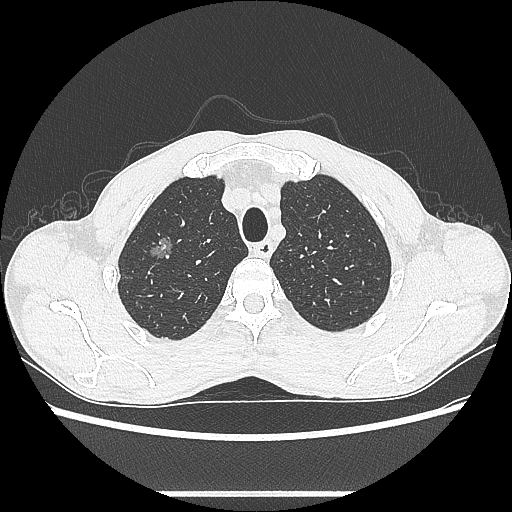
Chest CT, one axial slice. Reconstruction kernel LUNG. 100 kVp. Lung window (W 1500 / L -600 HU). 0.62 mm slice thickness. 512 × 512 image matrix, field of view 357 × 357 mm. Male patient, age 54 years. From the clinical record (not read from this slice): clinical TNM (as recorded): T1a N0 M0.
Structures marked on this image (rectangle marked by the reading radiologist):
- lung tumour (recorded histology: adenocarcinoma): bounding box <146,228,172,268> (left, top, right, bottom; pixels)